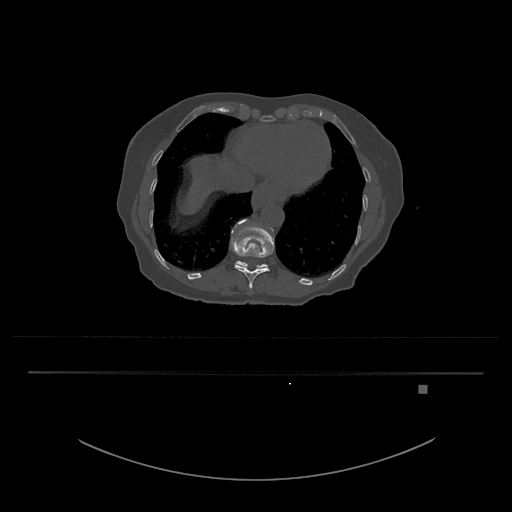
CT including the spine, one axial slice. Reconstruction kernel Br40s/3. 120 kVp. Bone window (W 1800 / L 400 HU). 512 × 512 image matrix, field of view 500 × 500 mm. Patient: female, 57 years. Case-level facts recorded for this patient, not image findings: primary cancer: cervical.
Structures marked on this image (semi-automatic segmentation, software-assisted and operator-edited):
- T11 vertebra: bounding box (x1, y1, x2, y2) in pixels: (230, 219, 274, 290)
- T12 vertebra: (235, 260, 268, 269)